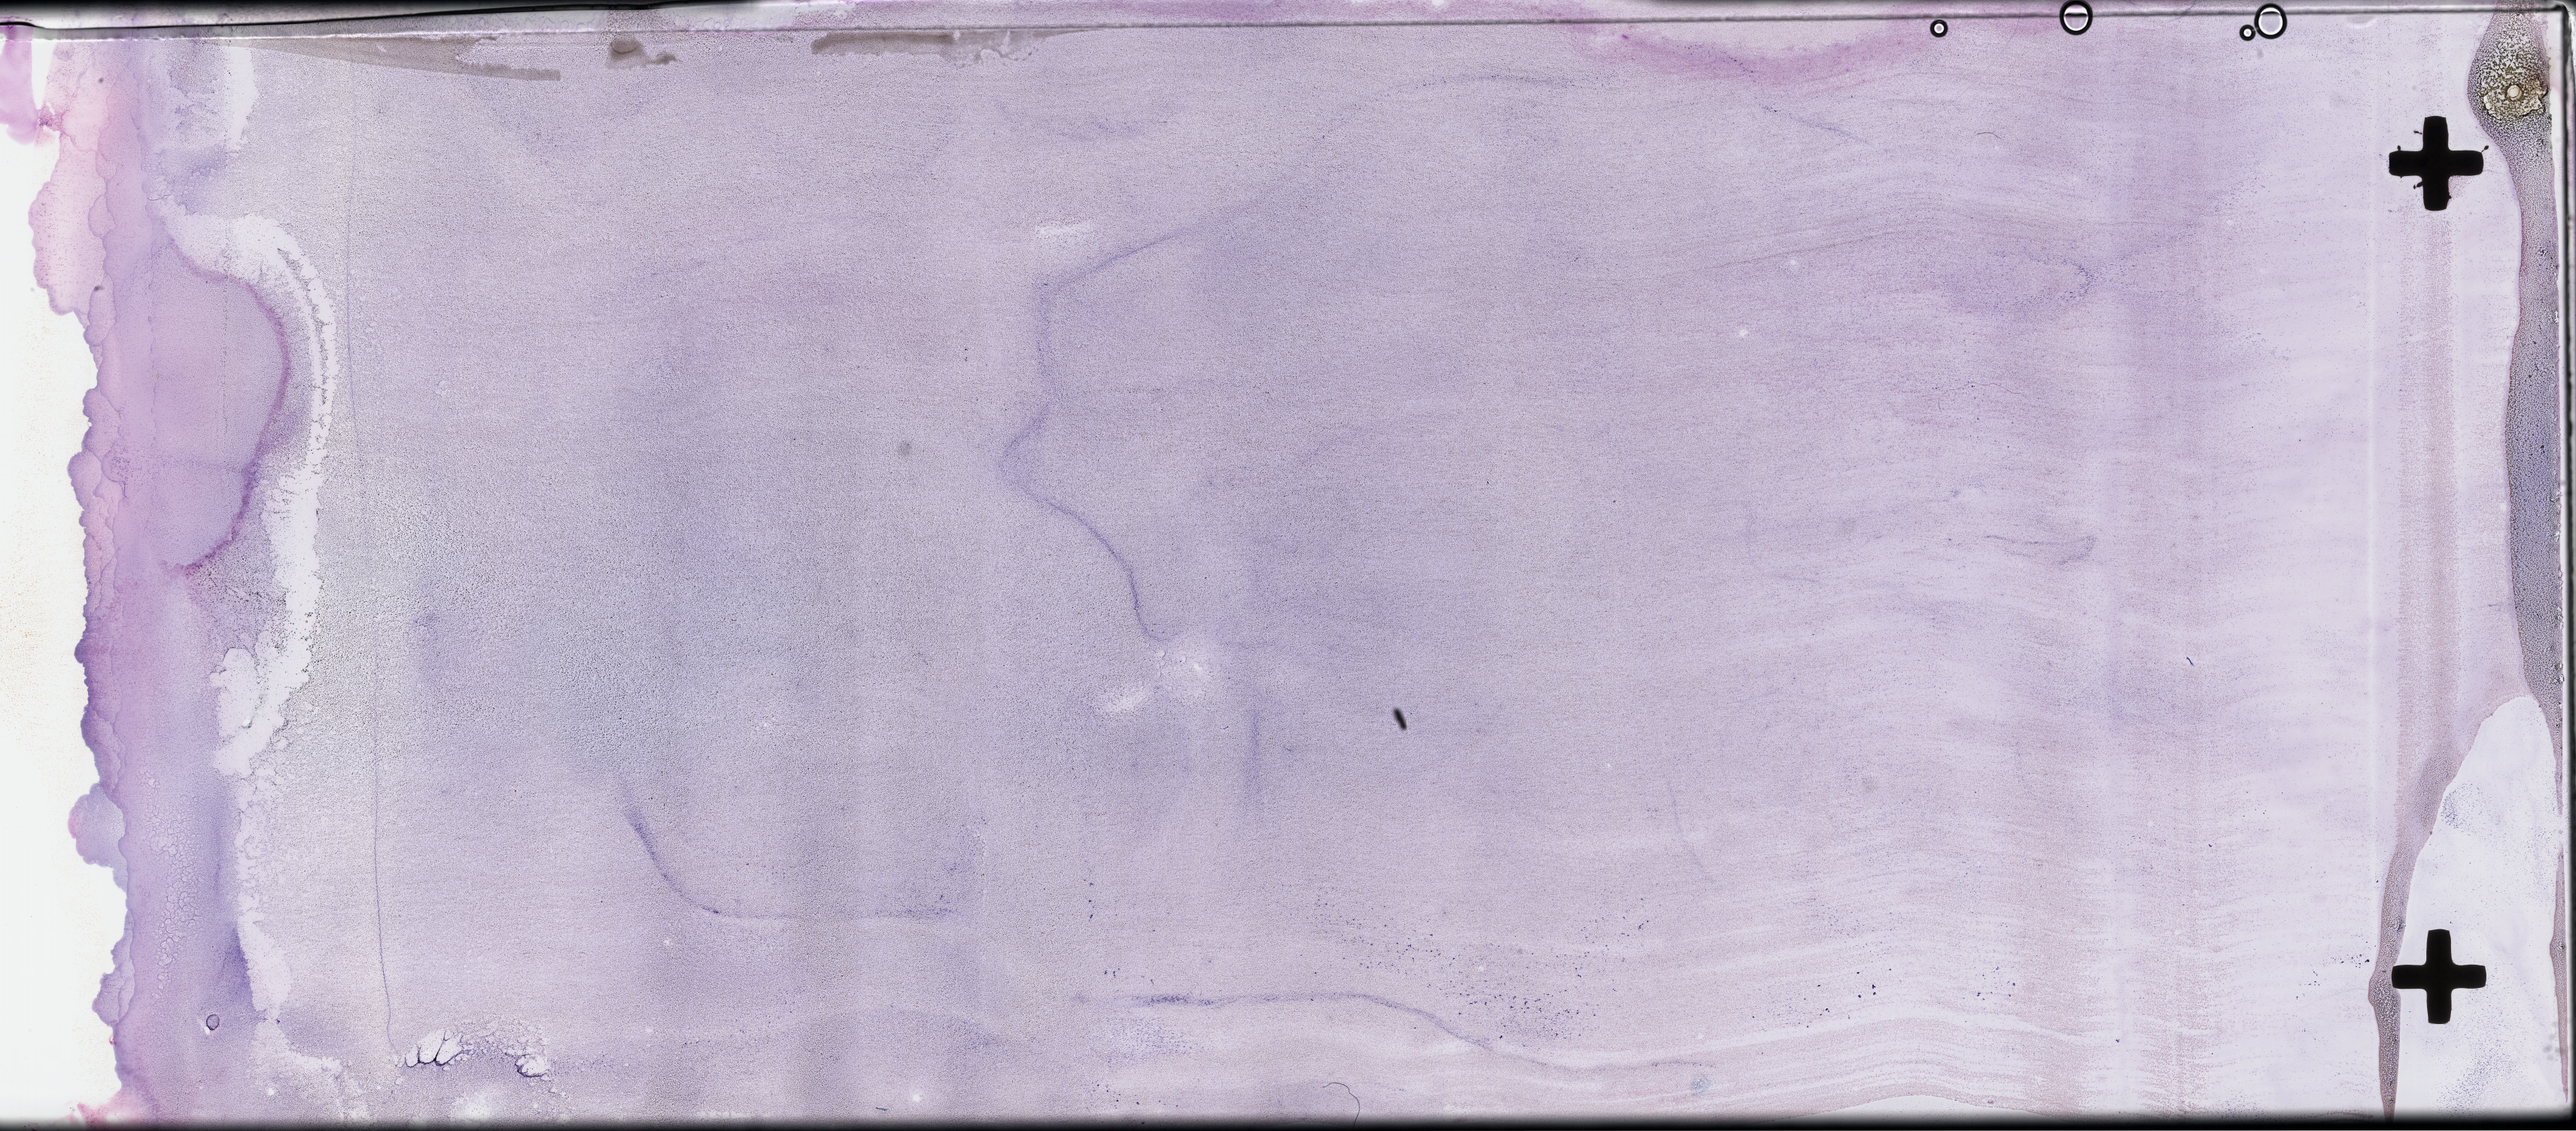
Whole-slide image of a whole blood smear, Wright-Giemsa stain, whole scanned area (about 55.3 x 24.3 mm) shown as a low-resolution overview. Patient sex: male.
Patient diagnosis: Plasma Cell Myeloma.